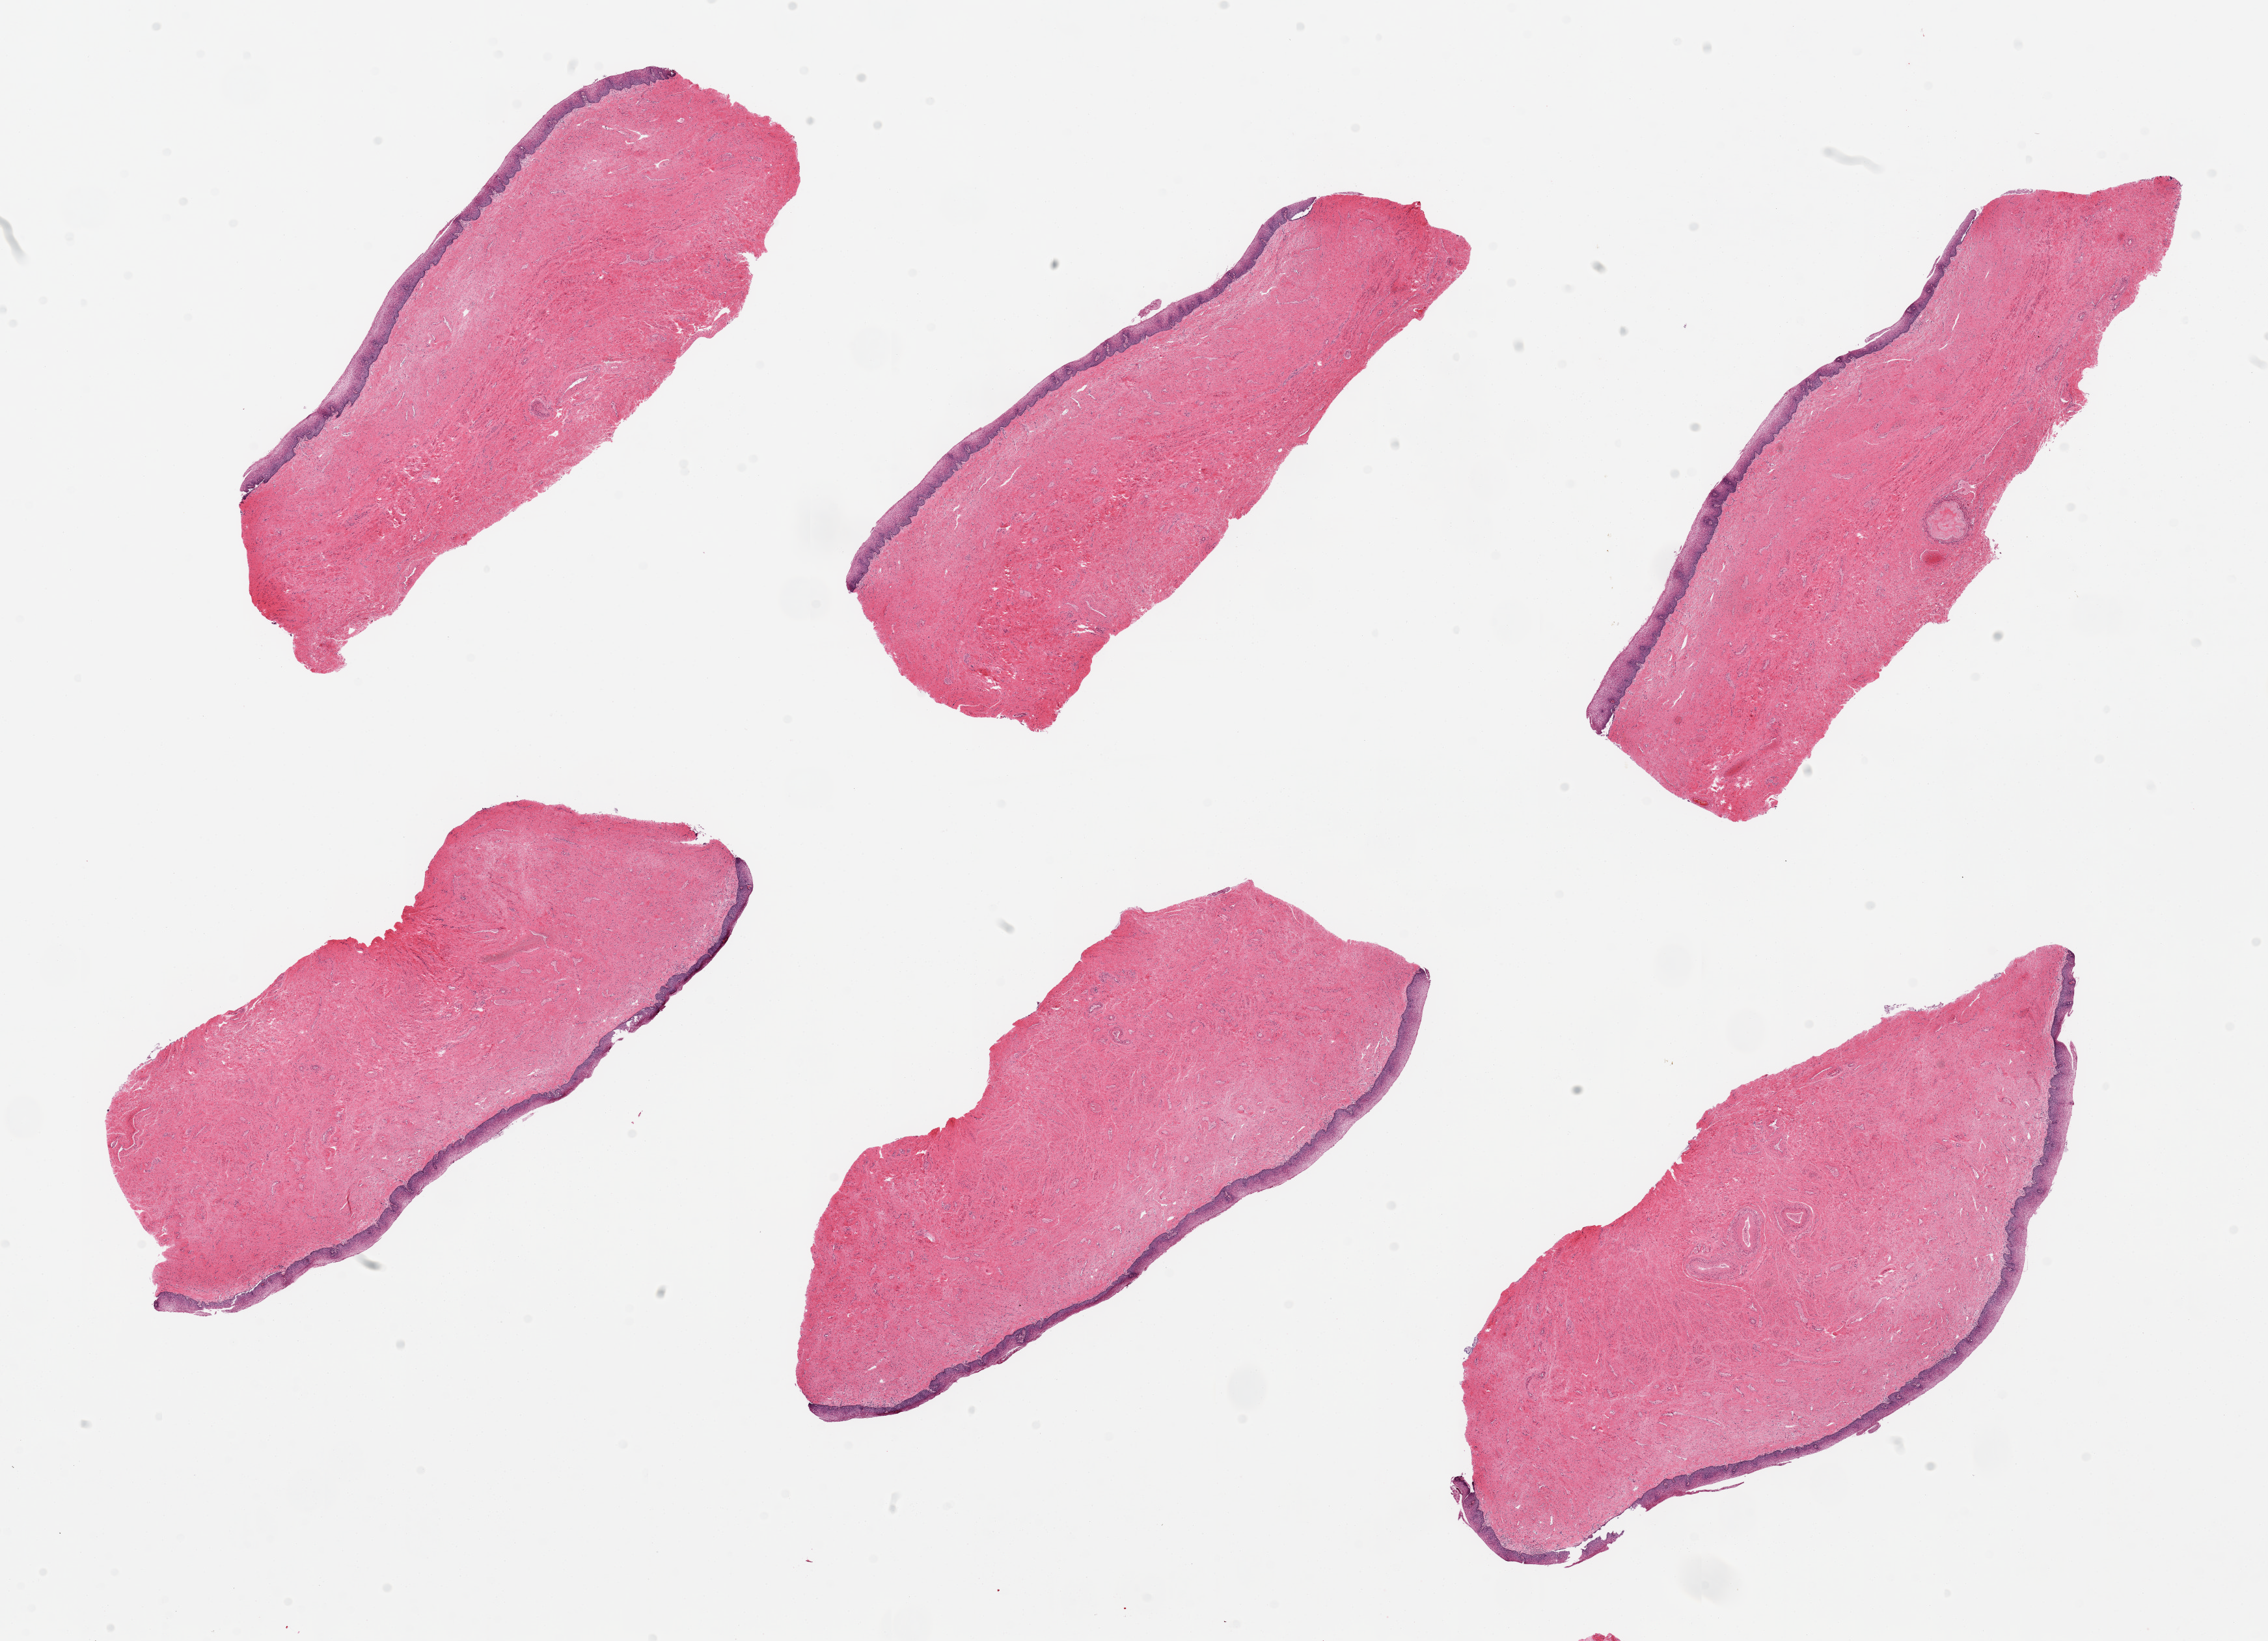
Haematoxylin and eosin whole-slide image, low-resolution overview of the scanned area, about 27.6 x 19.9 mm. PAXgene-fixed, paraffin-embedded tissue. Target tissue: vagina. Tissue donor sample. Donor sex: female.
* pathologist's review note for this sample: 6 pieces